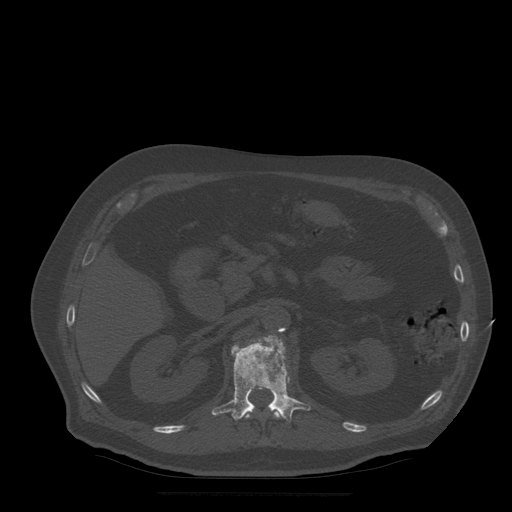
CT including the spine, one axial slice. Position 199 of 522 along the scan axis. Bone window (W 1800 / L 400 HU). 1.25 mm slice thickness. 512 × 512 image matrix, field of view 420 × 420 mm. Patient age 72 years. Case-level facts recorded for this patient, not image findings: primary cancer: prostate.
Structures marked on this image (semi-automatic segmentation, software-assisted and operator-edited):
- L1 vertebra: bounding box (x1, y1, x2, y2) in pixels: (212, 336, 311, 421)
- T12 vertebra: (246, 409, 280, 419)